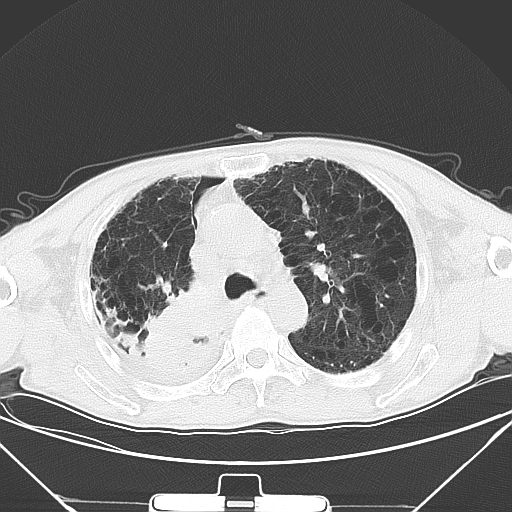
Chest CT, one axial slice; 120 kVp; lung window (W 1500 / L -600 HU); 5 mm slice thickness; 512 × 512 image matrix, field of view 373 × 373 mm. Patient: male, 65 years. Case-level facts recorded for this patient, not image findings: clinical TNM (as recorded): T3 N1 M1a.
Outlined on this slice (rectangle marked by the reading radiologist):
- lung tumour (recorded histology: squamous cell carcinoma): bounding box (x1, y1, x2, y2) in pixels: (135, 282, 226, 368)